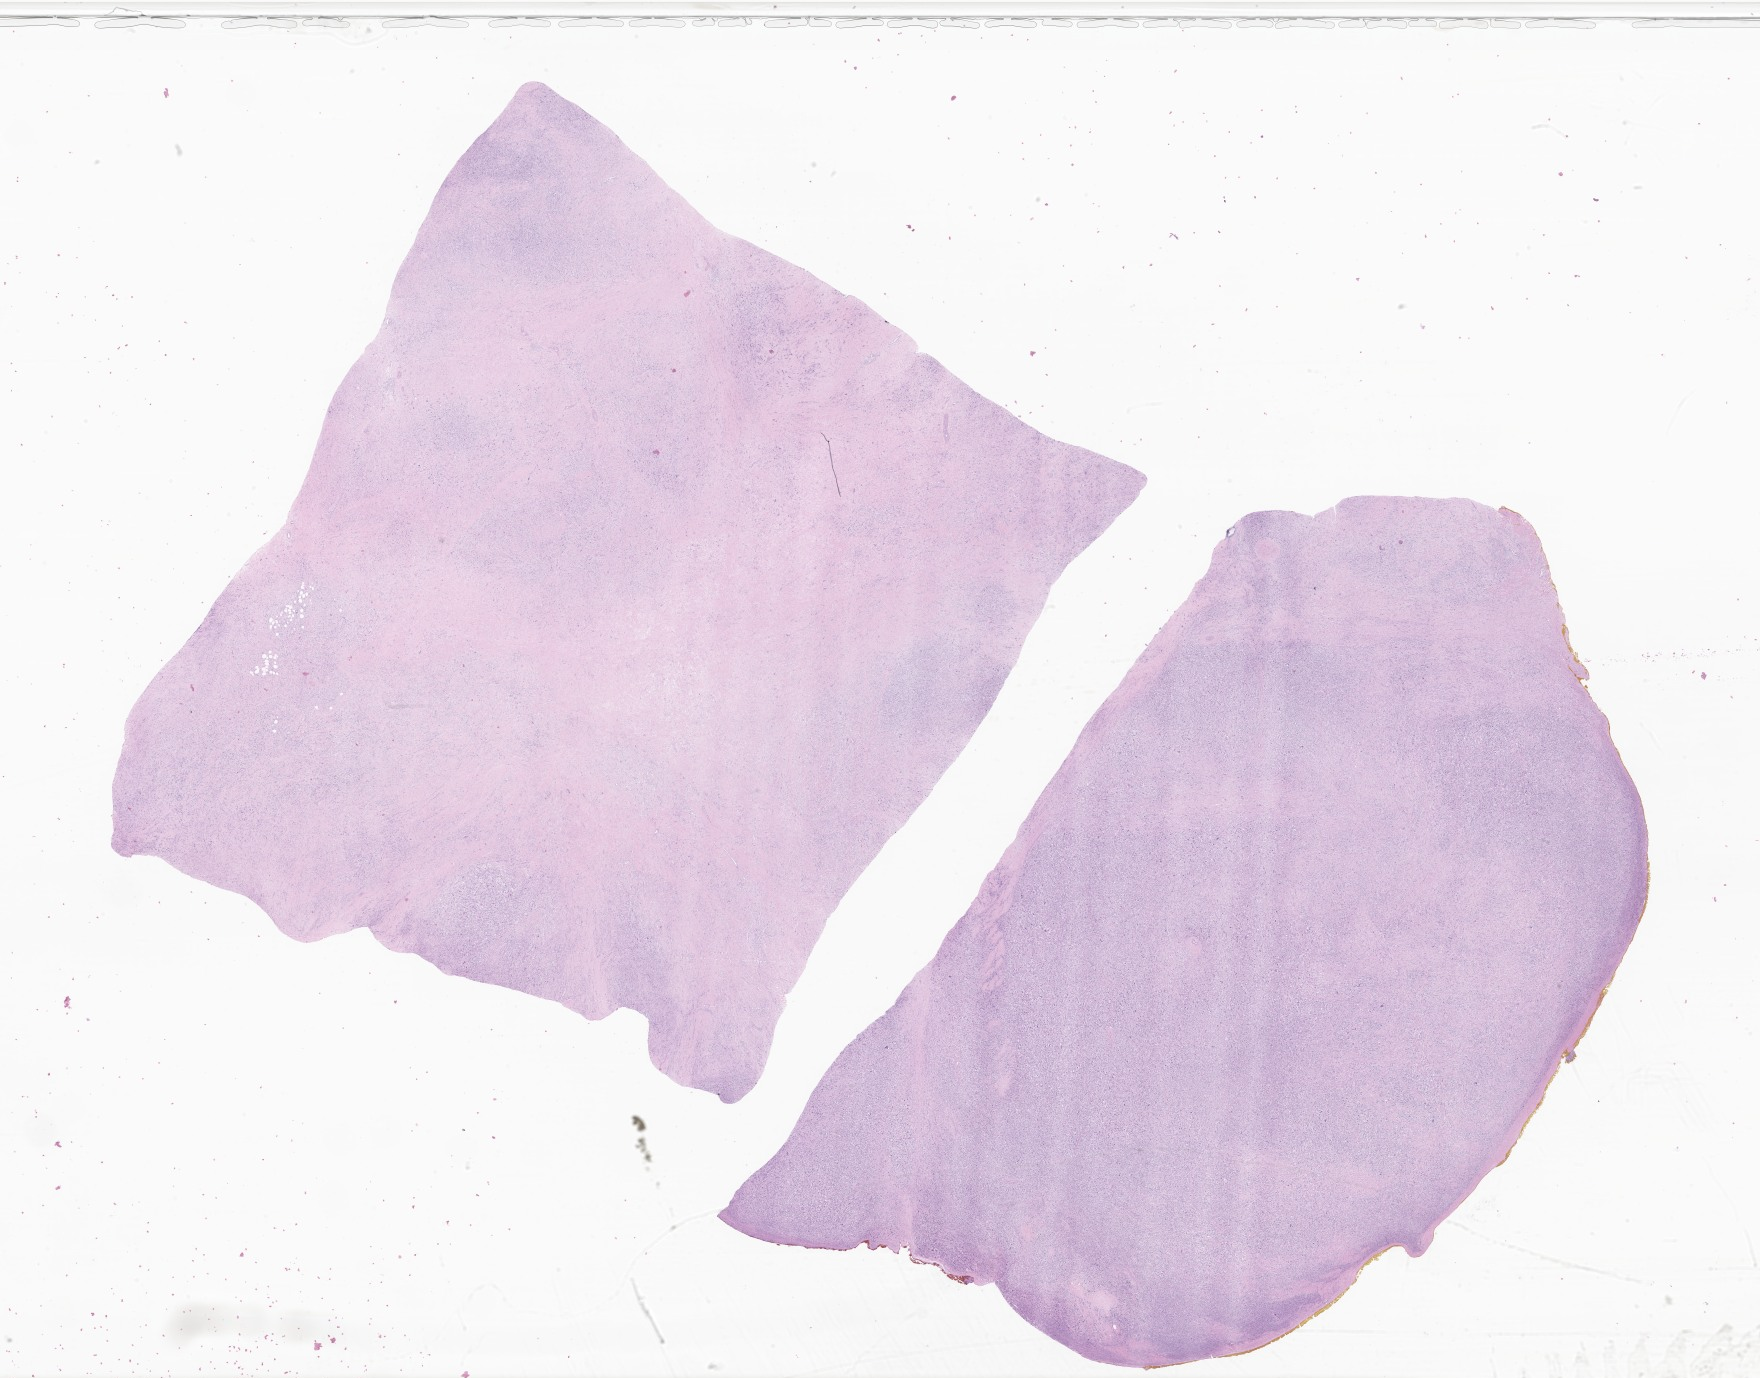
H&E whole-slide image of tumor tissue from the soft tissue of upper extremity, whole scanned area (about 29.7 x 23.2 mm) shown as a low-resolution overview, FFPE section. Male patient, age 747 days (about 2.0 years).
* diagnosis (ICD-O-3 morphology term): Rhabdomyosarcoma, NOS
* tissue or organ of origin (case record): connective, subcutaneous and other soft tissues of upper limb and shoulder